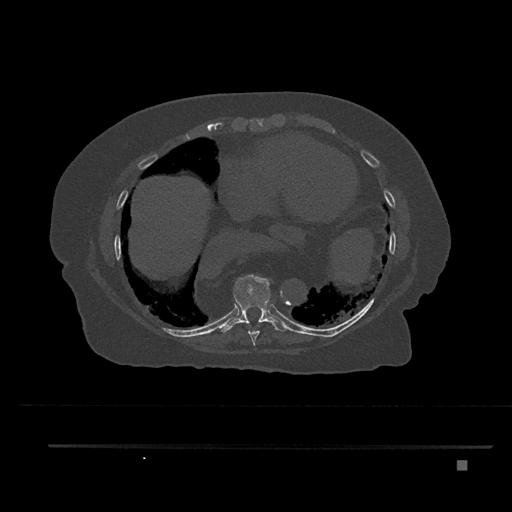
CT including the spine, one axial slice. Slice 416 of 797 in the series (ordered by position). Bone window (W 1800 / L 400 HU). 0.5 mm slice thickness. 512 × 512 image matrix, field of view 437 × 437 mm. Female patient, age 76 years. From the clinical record (not read from this slice): primary cancer: lung.
Annotated regions visible in this slice (semi-automatic segmentation, software-assisted and operator-edited):
- T8 vertebra: bounding box <248,330,260,346> (left, top, right, bottom; pixels)
- T9 vertebra: <220,275,289,333>